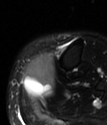
MRI of an extremity soft-tissue mass, one axial slice; position 22 of 78 along the scan axis; T2-weighted fat-saturated; MR volume resampled by the dataset authors to the PET/CT grid (not the native acquisition matrix); 3.27 mm slice thickness; 107 × 125 image matrix, field of view 104 × 122 mm. Female patient. From the clinical record (not read from this slice): histological type: extraskeletal high grade osteogenic sarcoma; grade: high; site of the primary tumour: left calf.
Structures marked on this image (expert contour drawn on MRI and transferred to this co-registered scan by the dataset authors):
- gross tumour volume (mass): bounding box [x1, y1, x2, y2] px = [23, 54, 56, 99]